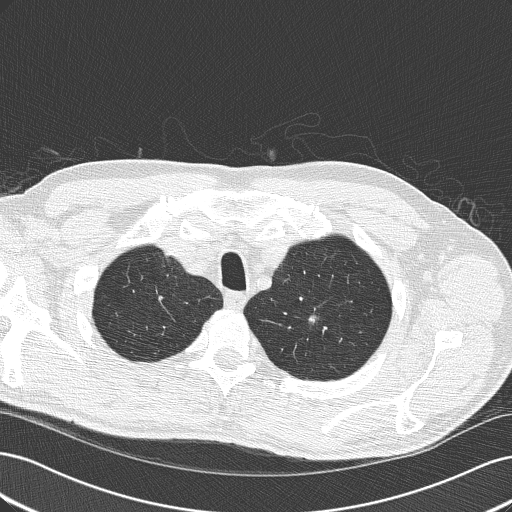
Axial slice from a low-dose chest CT screening exam; third screening round (two years after baseline); lung window (W 1500 / L -600 HU); lung (sharp) reconstruction kernel (B50f); 512 × 512 image matrix. Male participant, aged 64 years at enrolment.
Expert-annotated lung lesion, box from (x=288, y=297) to (x=336, y=343) px. Reader record for this screening exam (exam-level; its link to the box is not recorded): non-calcified nodule or mass ≥4 mm, left upper lobe, 8 × 8 mm, smooth margins, soft tissue attenuation, pre-existing on the prior screen: yes; interval growth: yes. Official screen result: positive, other. Participant outcome: lung cancer diagnosed 111 days after this screen — adenocarcinoma, NOS, left upper lobe, poorly differentiated (G3), stage IA (AJCC 6th edition), 10 mm at pathology.